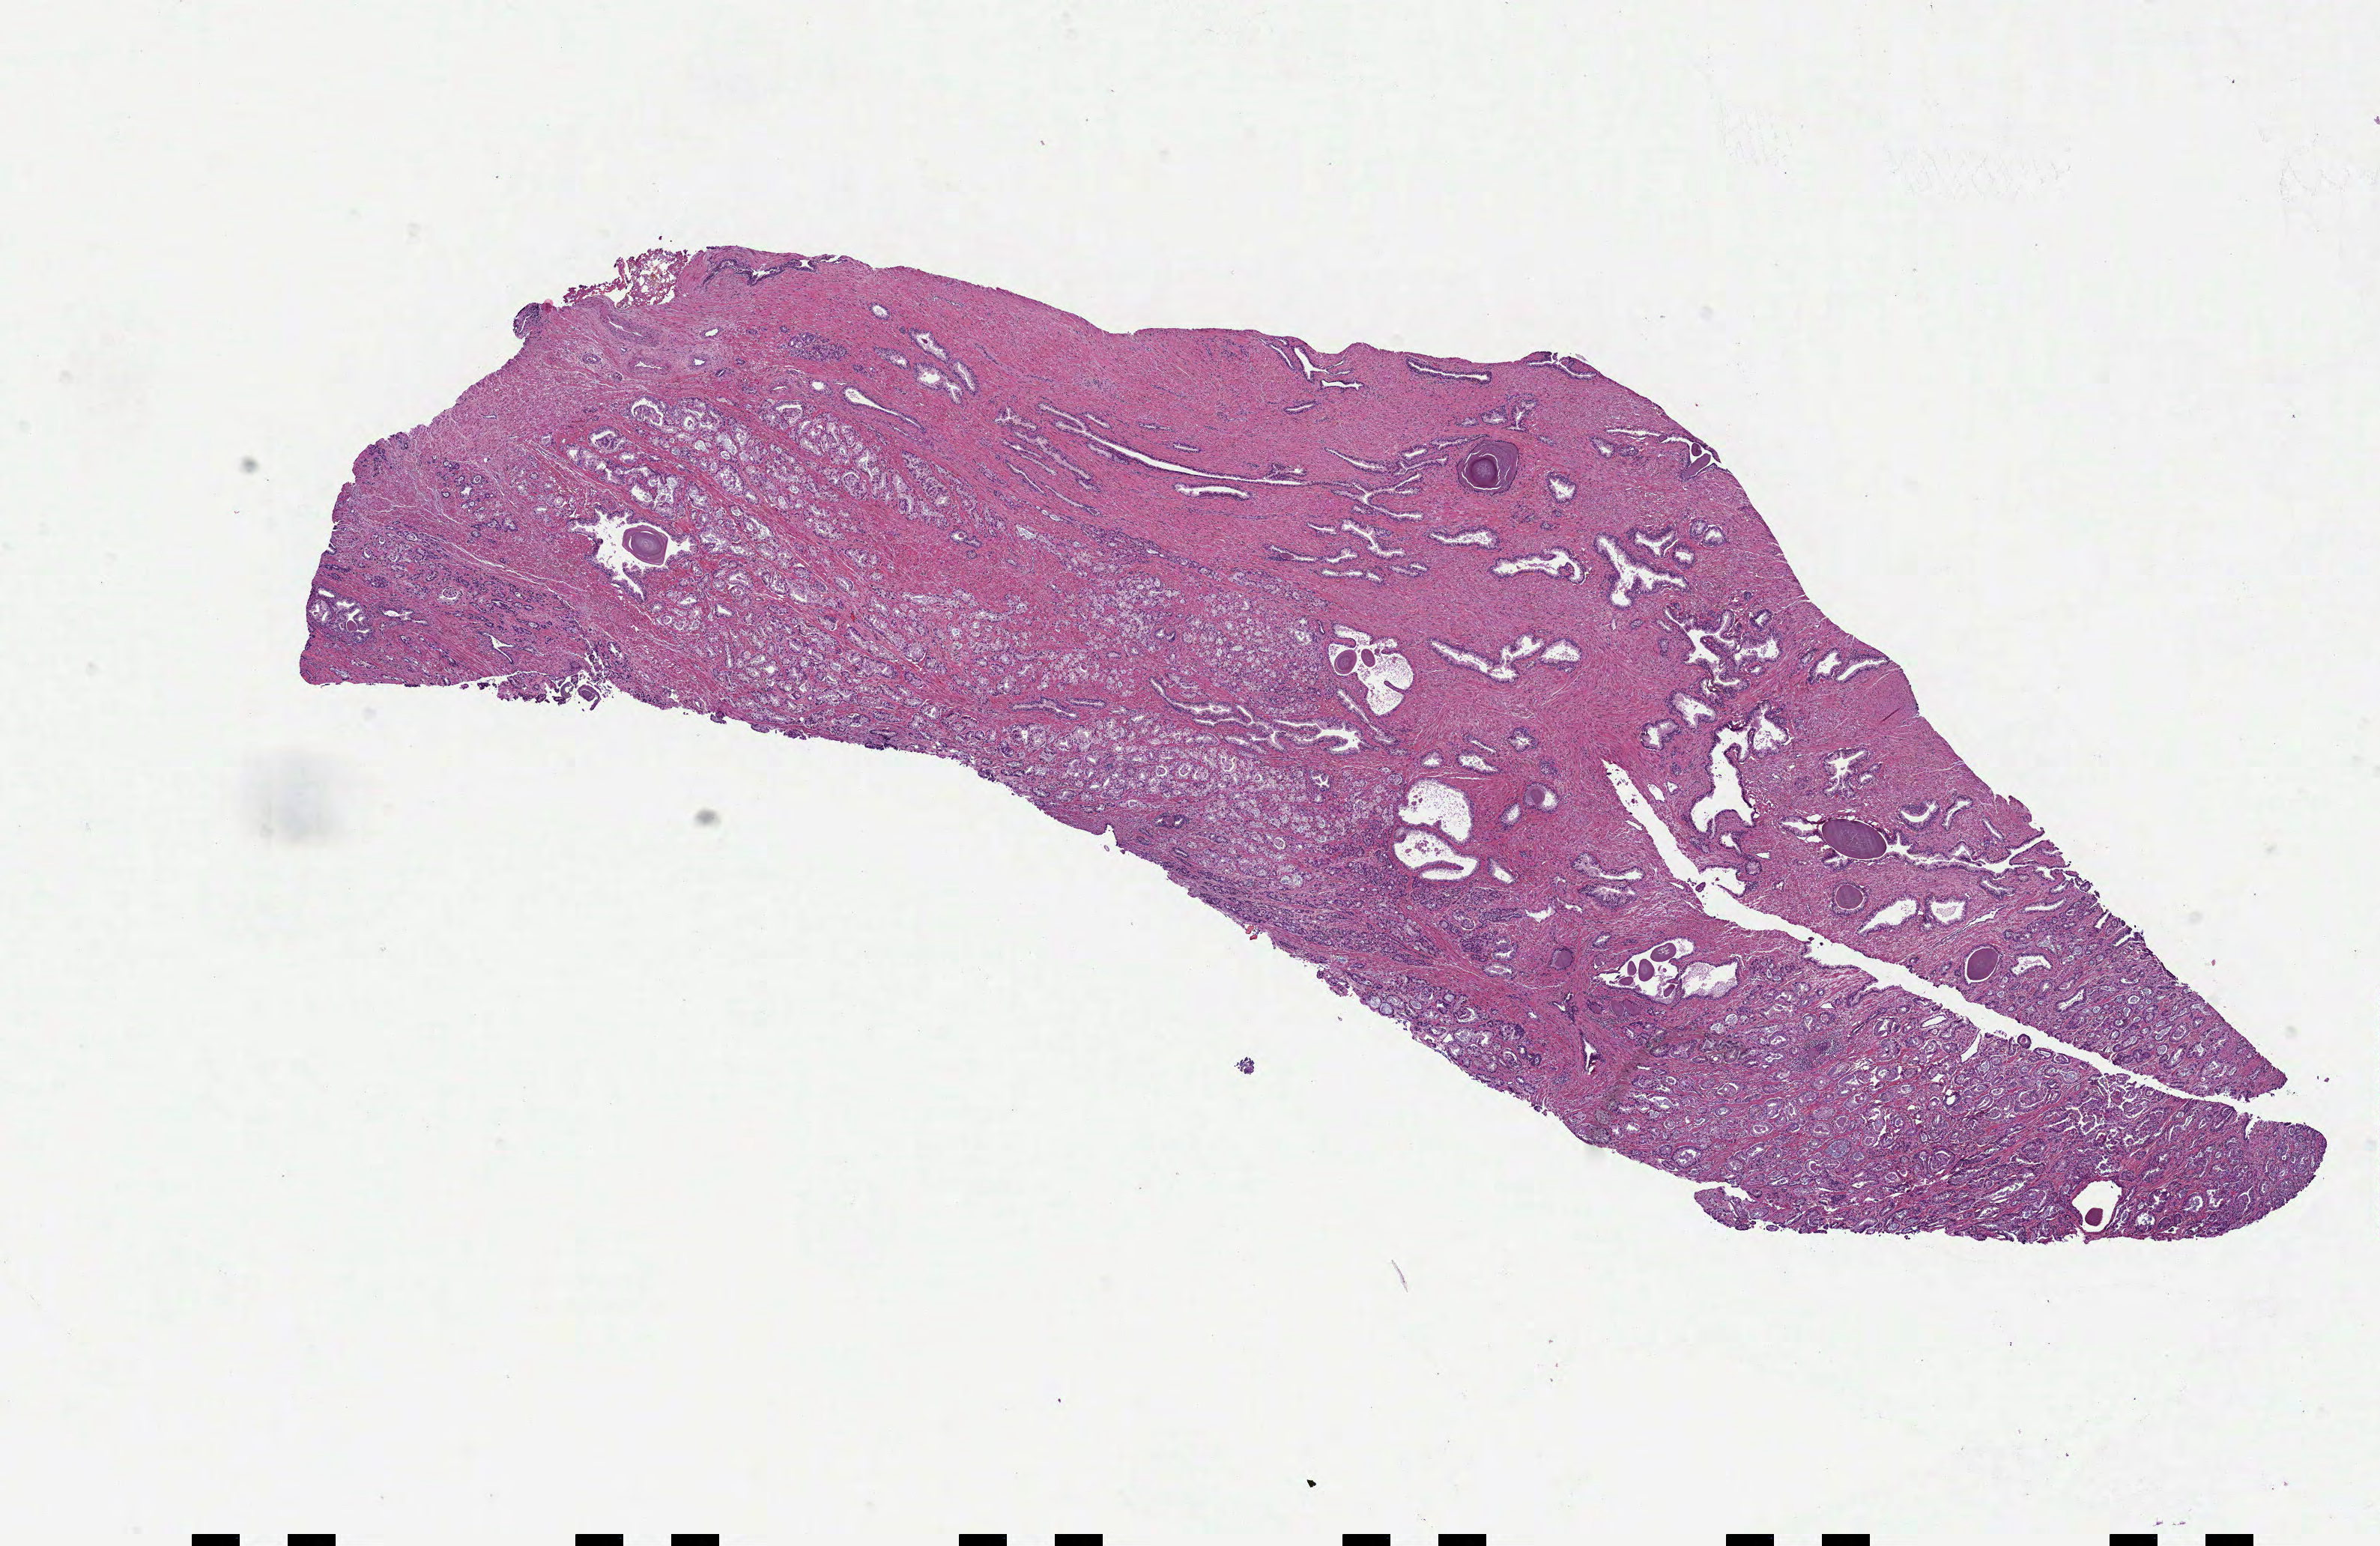
H&E-stained whole-slide image — shown as a low-resolution overview of the whole scanned area (about 12.8 x 8.3 mm, slide scanned at 40x), FFPE section, sample: primary tumour, prostate. Patient: male, age at initial diagnosis 61 years. Gleason score: 7 (3+4).
Laterality: bilateral. Diagnosis: Acinar cell carcinoma.